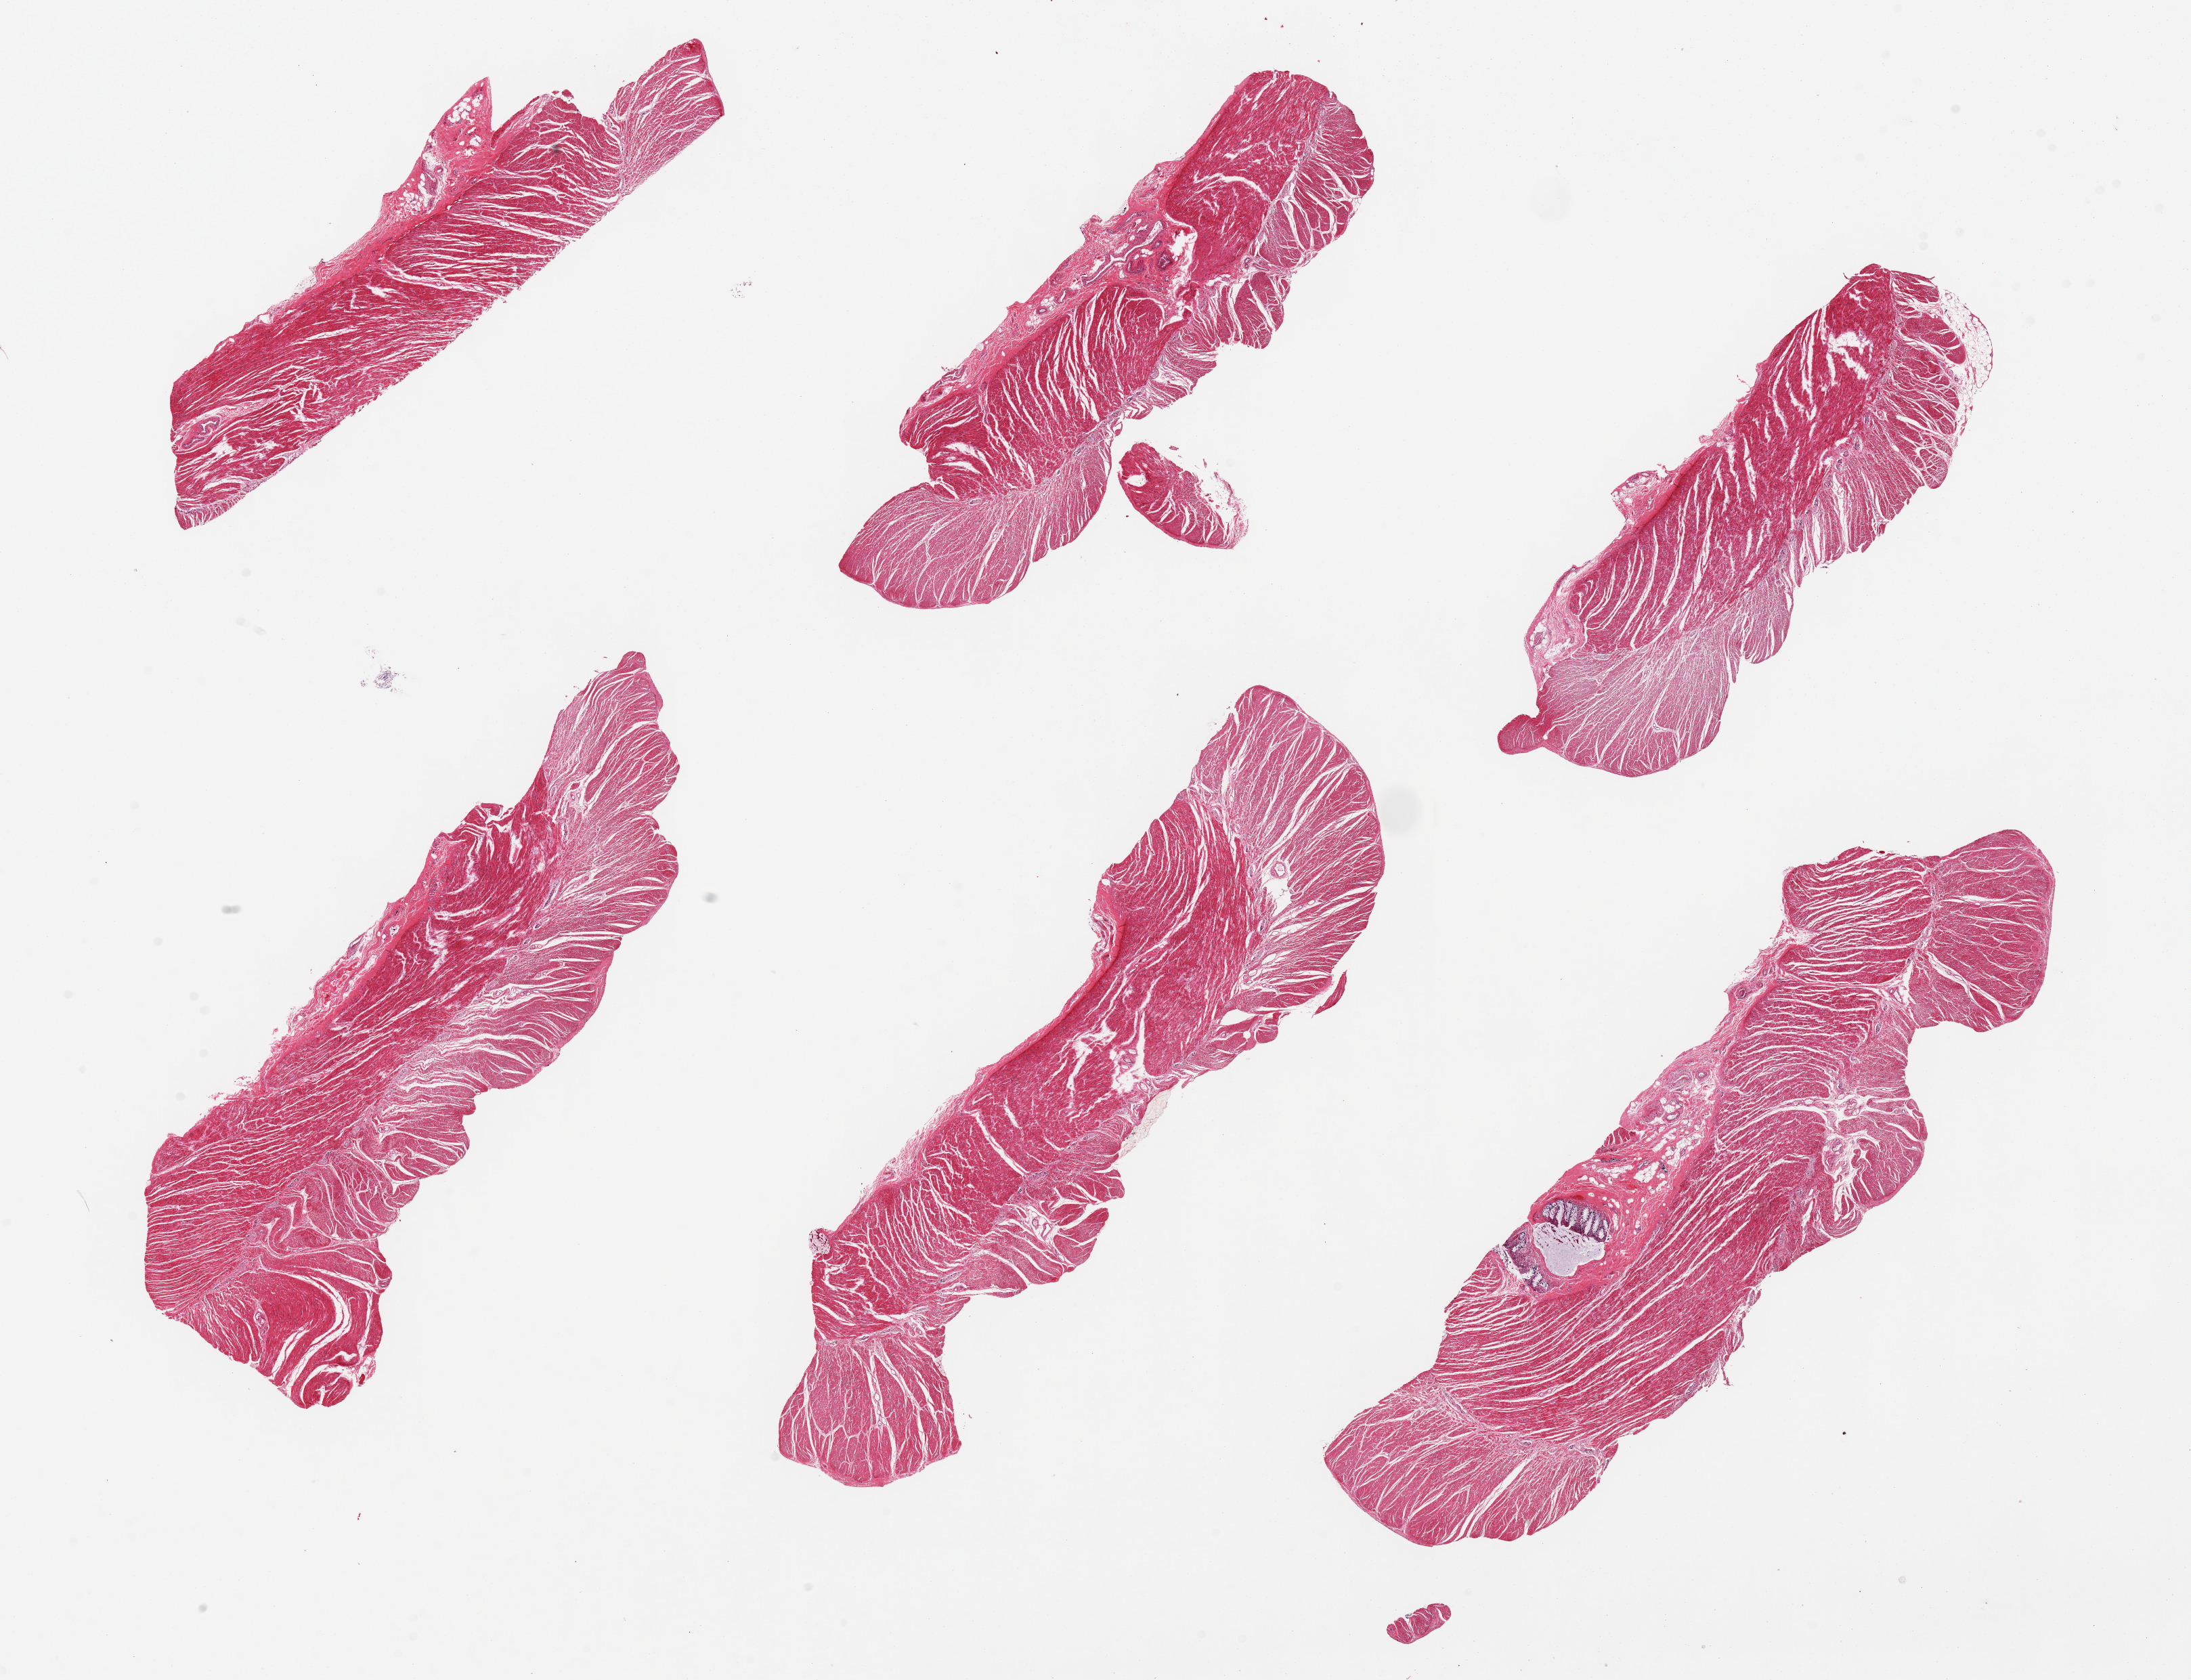
Digitized haematoxylin and eosin-stained section — low-resolution overview of the scanned area, about 25.6 x 19.6 mm (from a 20x scan); PAXgene-fixed paraffin-embedded (PFPE) section; target tissue: sigmoid colon; tissue donor sample. Donor: female.
• pathologist's review note for this sample: 6 pieces, all muscularis except focal mucosal diverticulum; unusually poorly preserved, focal areas advance autolysis